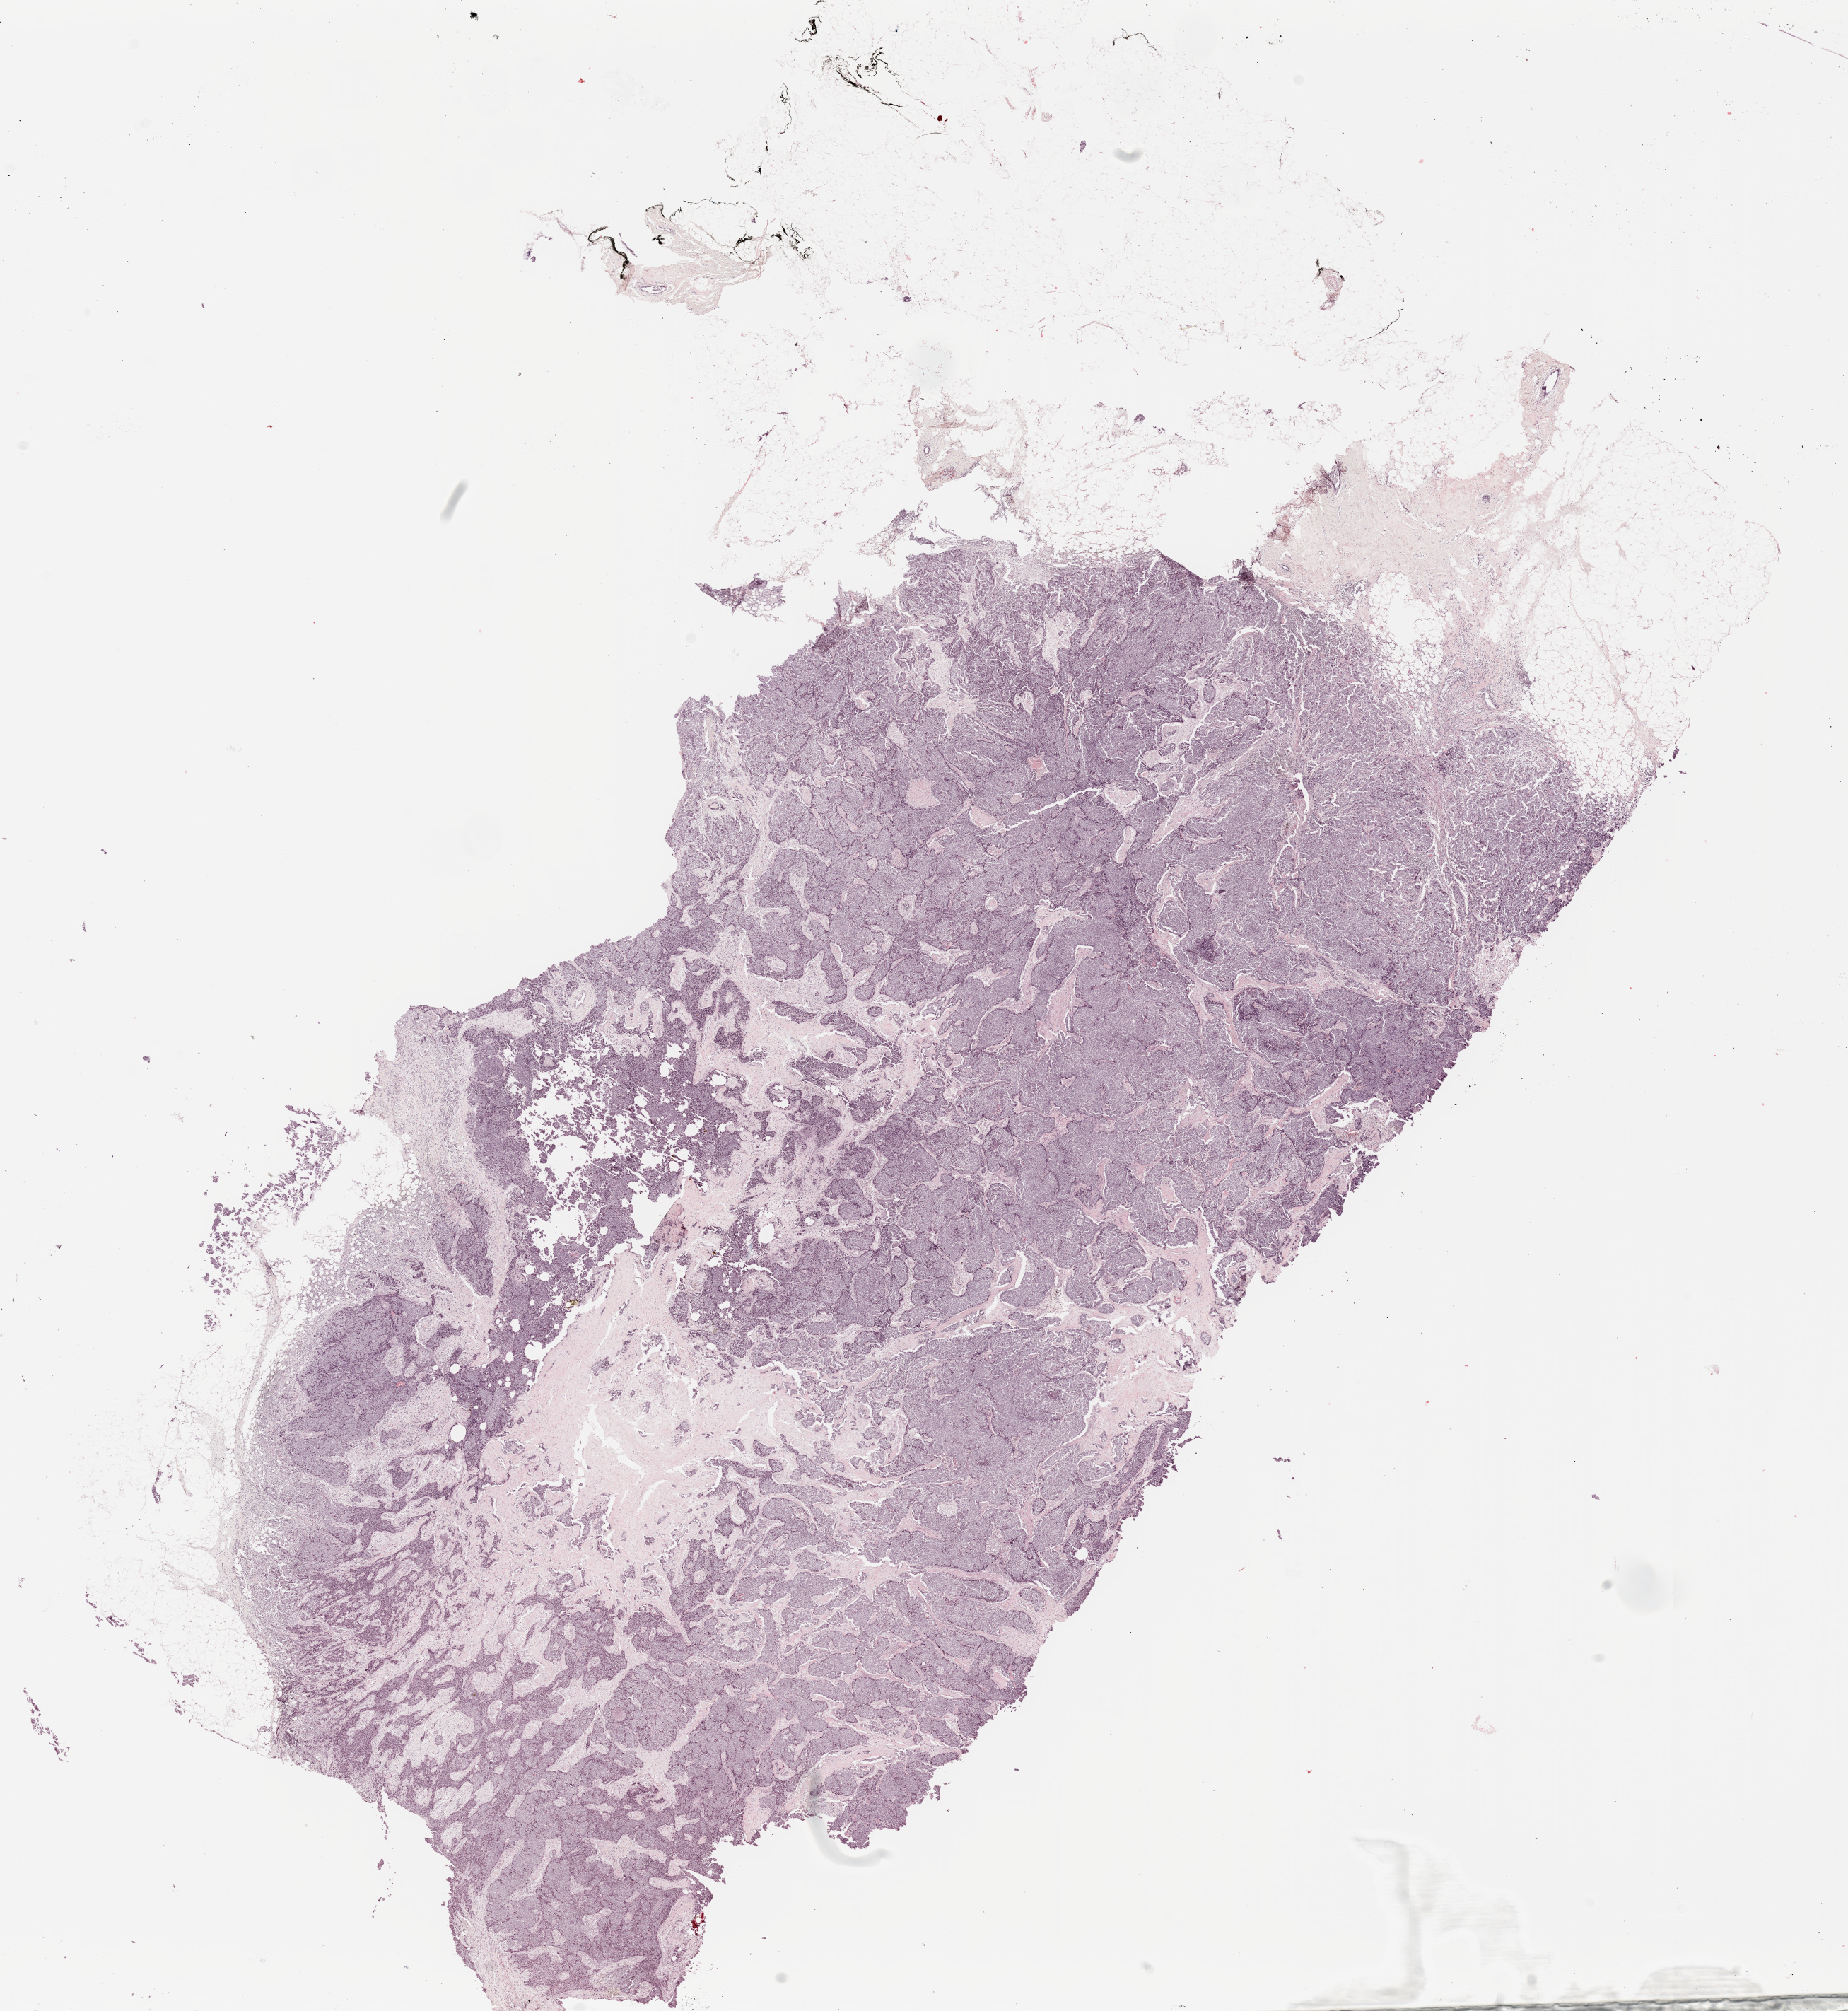
Digitized Hematoxylin and eosin (H&E) stained tissue section (whole slide), a low-resolution overview of the entire scanned area, about 20.9 x 22.7 mm (acquisition: 20x scan); formalin-fixed paraffin-embedded (FFPE) diagnostic section; primary tumour sample from the breast. Patient: female, age at initial diagnosis 54 years.
Laterality: right. AJCC pathologic stage: IIB (6th edition). Pathologic diagnosis: Infiltrating duct carcinoma, NOS. TNM: T2 N1 M0.